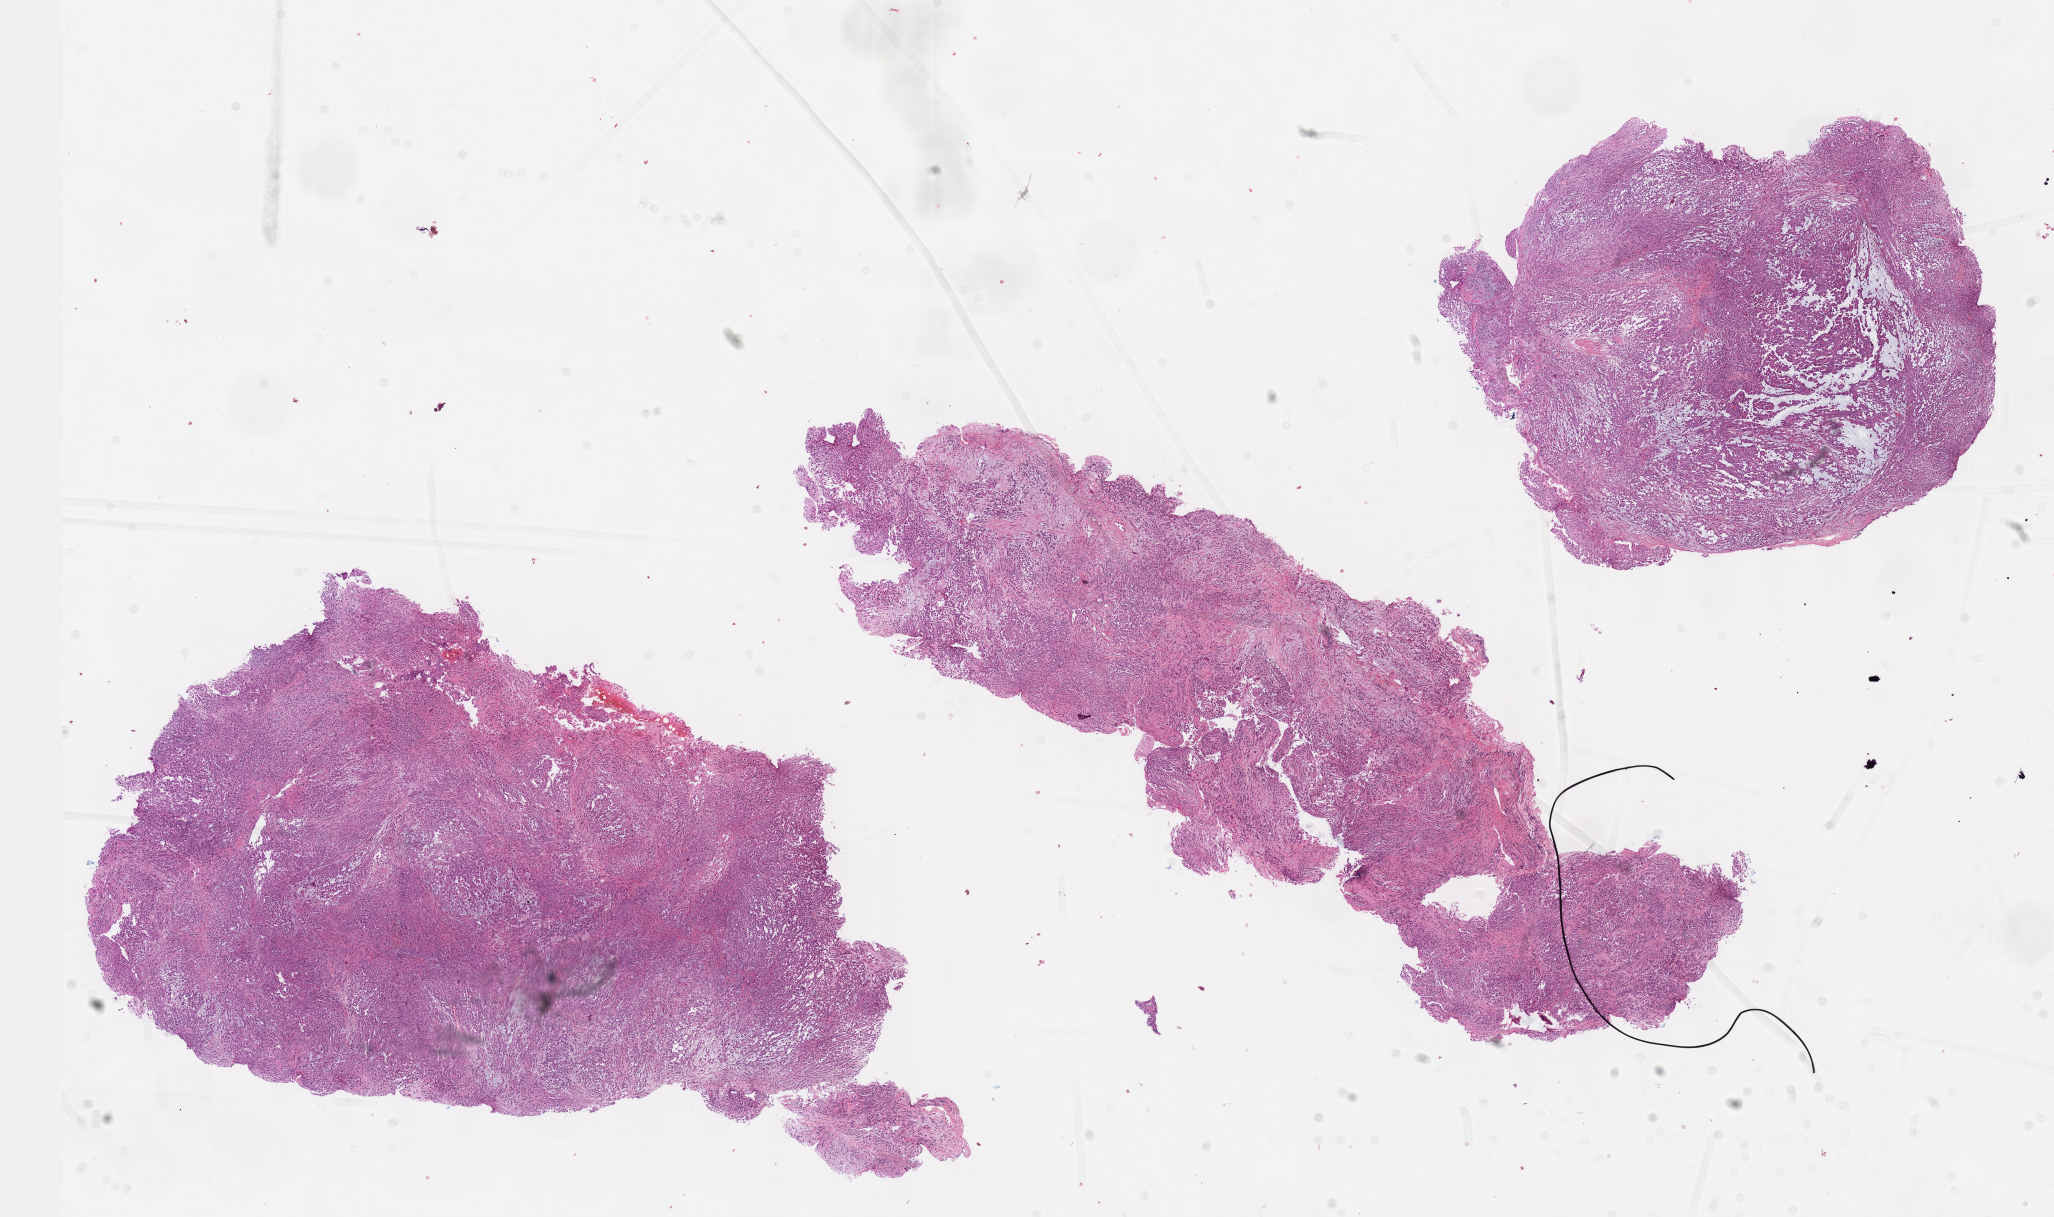
H&E-stained whole-slide image — low-resolution overview of the scanned area, about 16.6 x 9.8 mm. Formalin-fixed paraffin-embedded (FFPE) diagnostic section. Primary tumour sample from the mesothelium. Male, age 74 years at initial diagnosis.
* histologic diagnosis: Epithelioid mesothelioma, malignant (pleura, NOS)
* AJCC pathologic stage: I (7th edition)
* TNM: T1 N0 M0